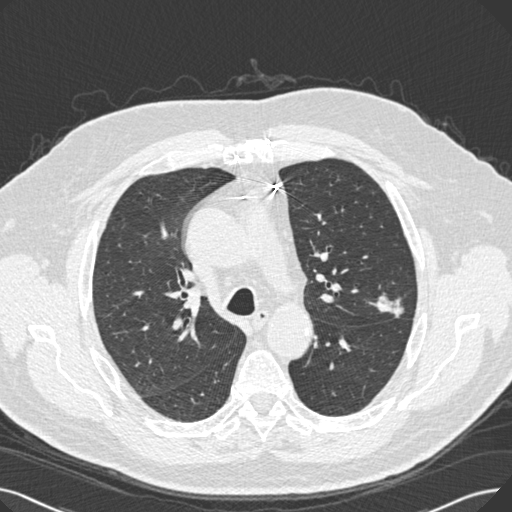
Low-dose screening chest CT, one axial slice; slice 177 of 269 in the series (ordered by position); reconstruction kernel B30f; lung window (W 1500 / L -600 HU); 512 × 512 image matrix.
Annotated regions visible in this slice (outlined manually by an expert reader):
- lesion 1 (tumor, upper lobe of left lung): bounding box <373,288,404,318> (left, top, right, bottom; pixels)